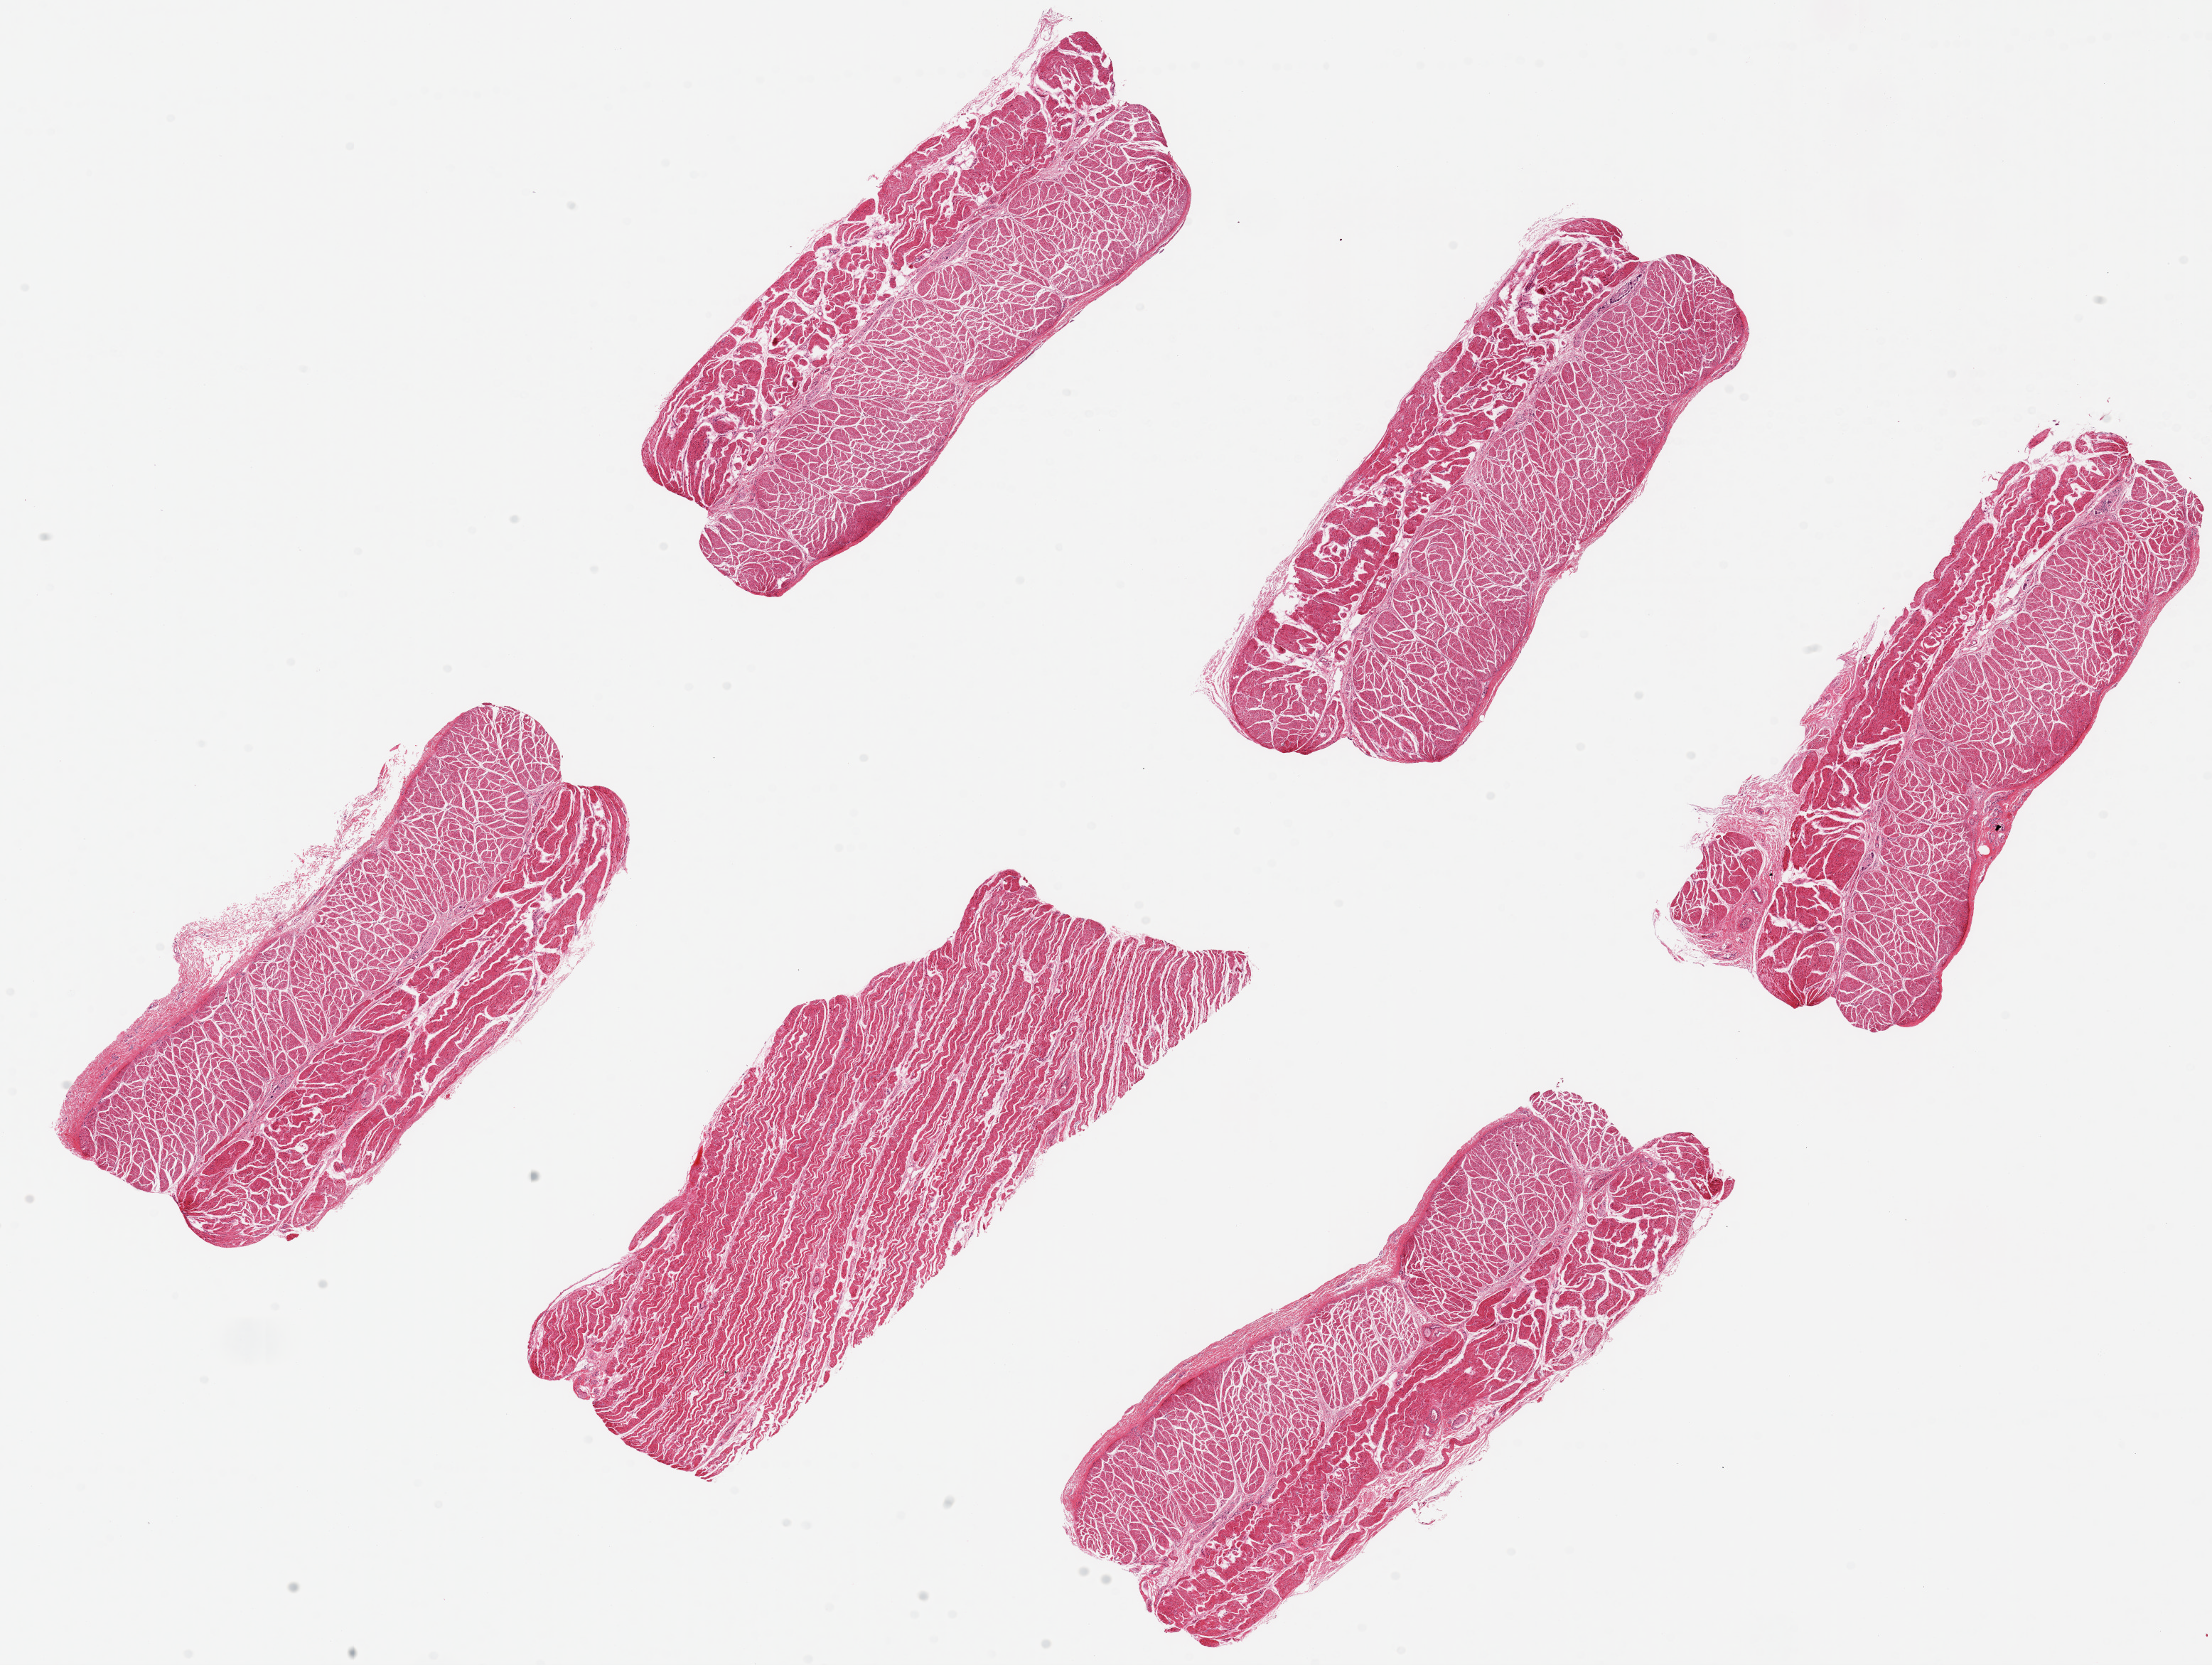
Digitized hematoxylin and eosin (H&E)-stained section — low-resolution overview of the scanned area, about 24.6 x 18.5 mm (from a 20x scan). PAXgene-fixed paraffin-embedded (PFPE) section. Sampled site (target tissue): esophageal muscle. Donor tissue sample. Donor: male.
Reviewer comment on this tissue sample: 6 pieces ~7x2.5mm, all muscularis.